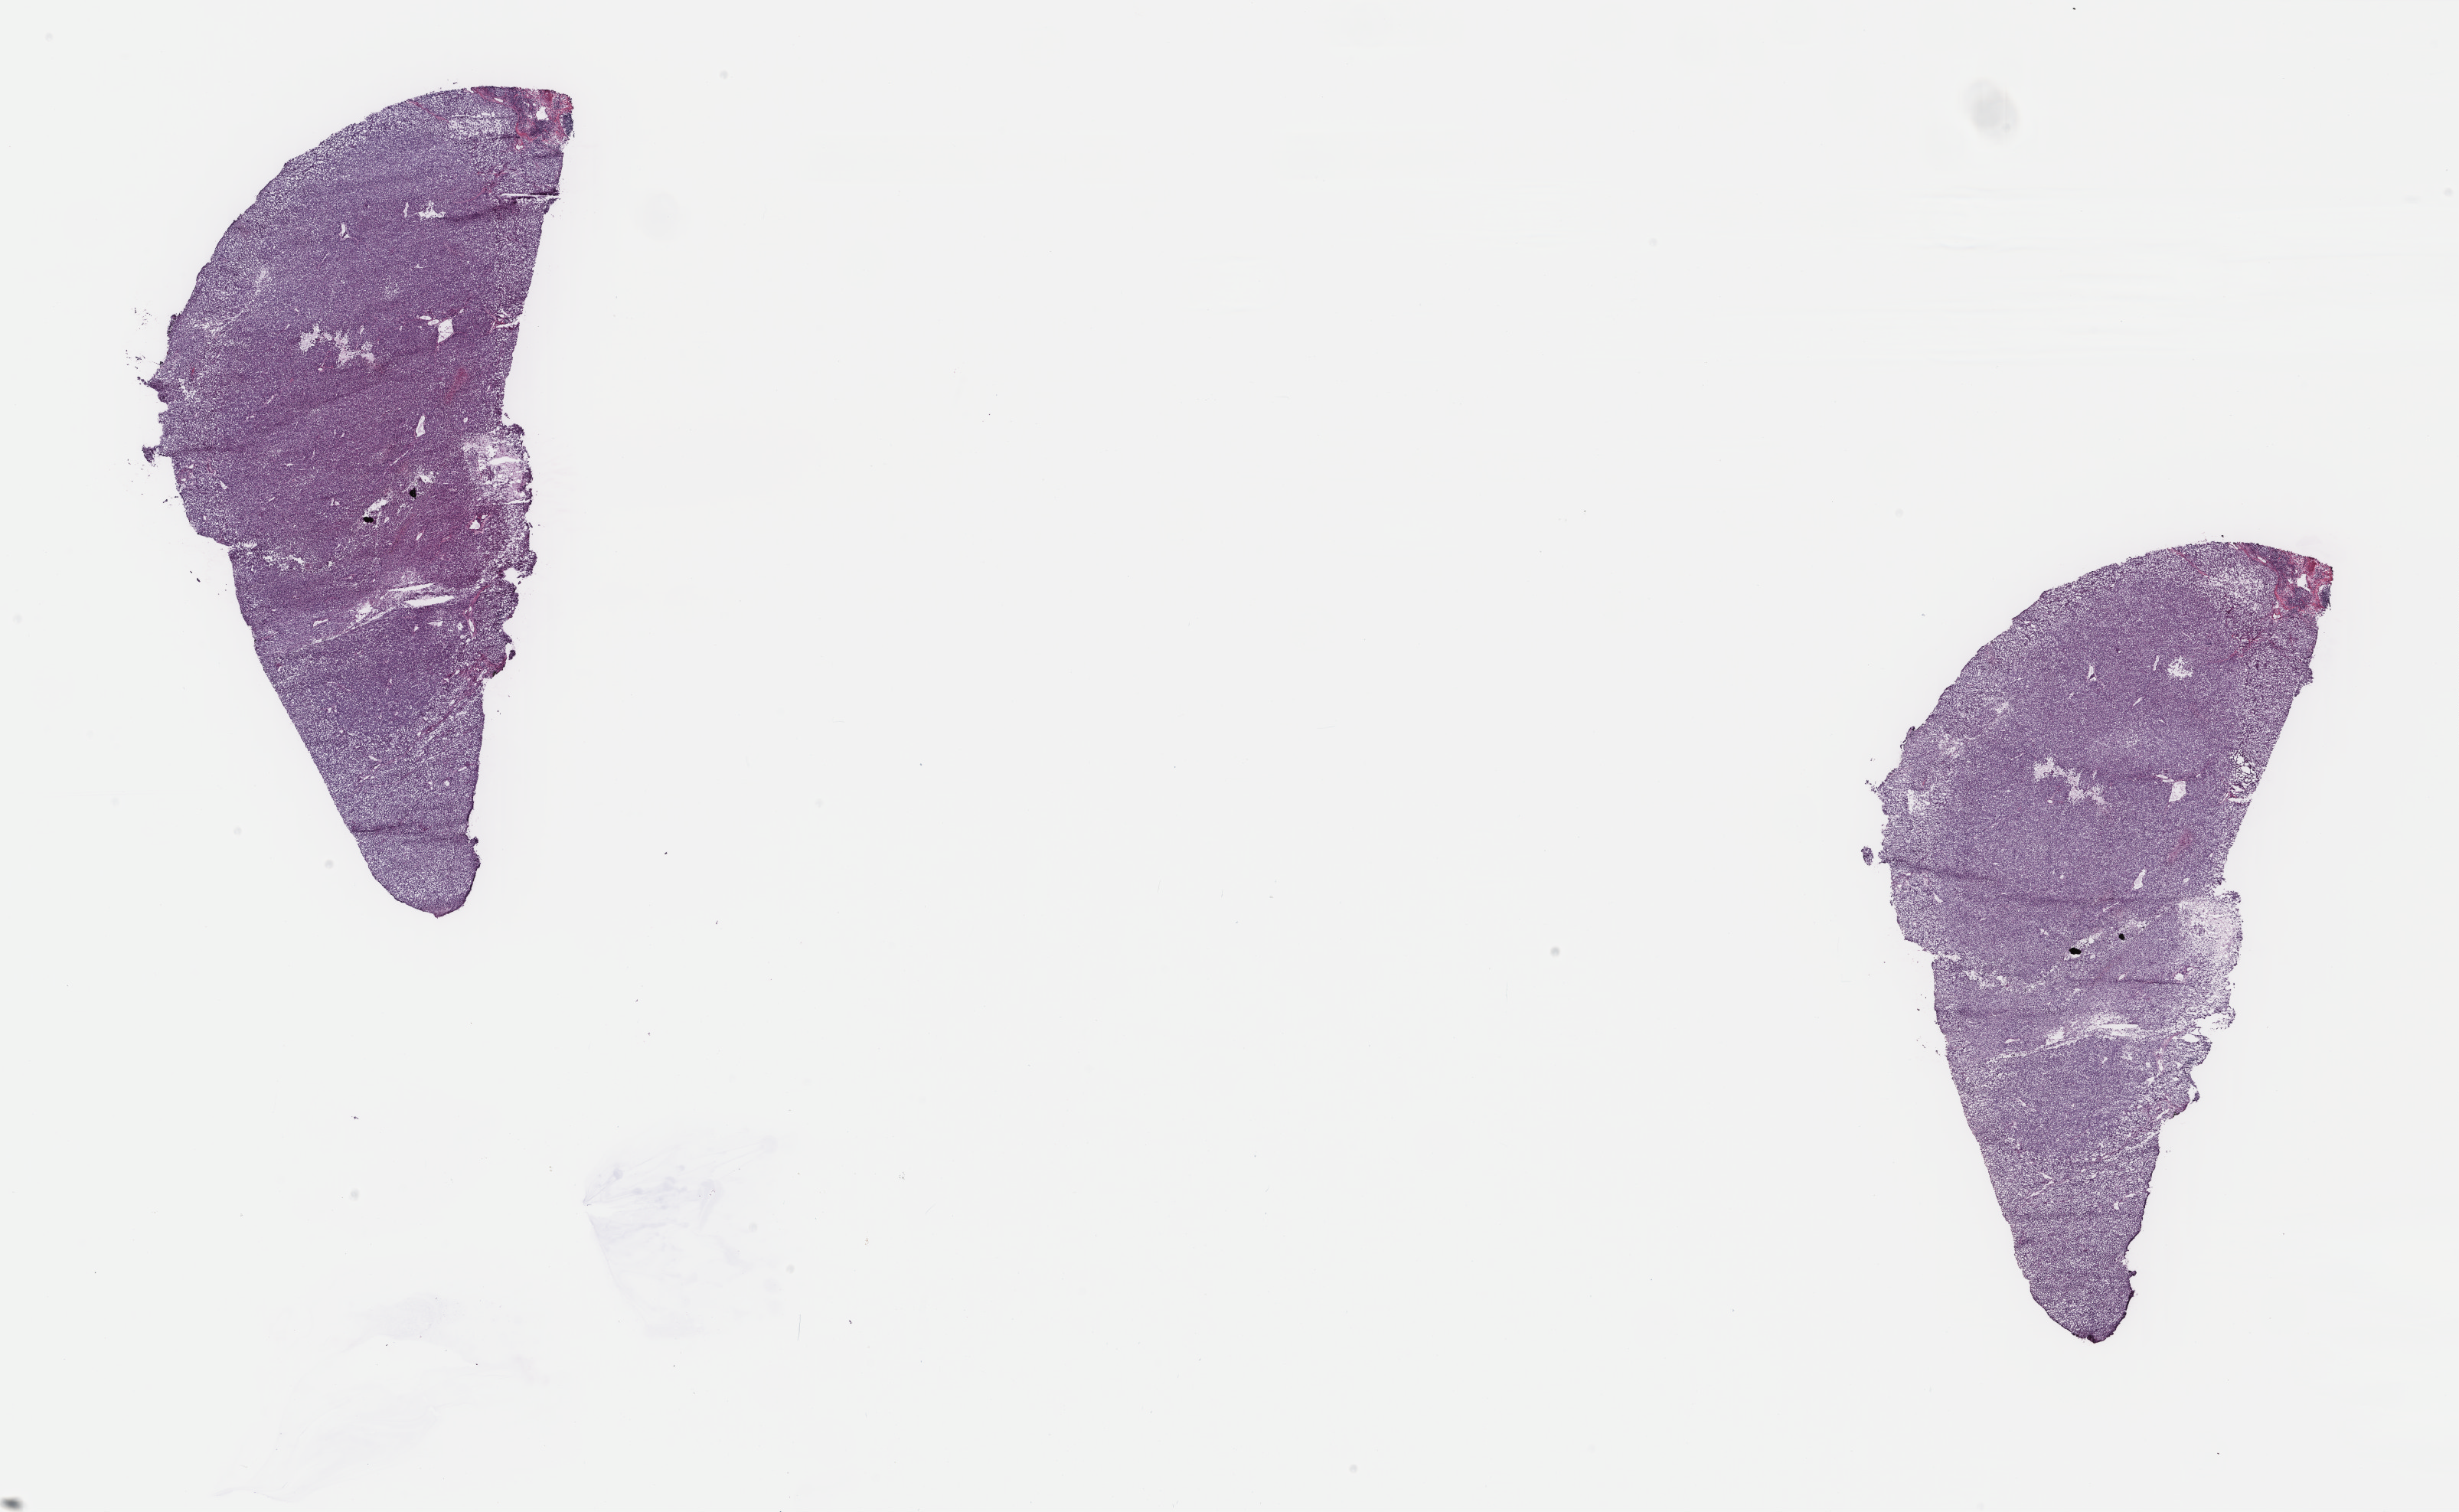
Digitized Hematoxylin and eosin (H&E) stained tissue section (whole slide) — a low-resolution overview of the entire scanned area, about 25.5 x 15.7 mm (acquisition: 40x scan); frozen section from the top of the tissue portion; metastatic tumour sample. Patient: male, age at initial diagnosis 30 years. Composition of this section per pathologist review: tumour cells 98%, tumour nuclei 97%, normal cells 0%, stromal cells 0%, necrosis 2%. Infiltration values recorded for this section: lymphocyte infiltration 0%, monocyte infiltration 0%, neutrophil infiltration 0%.
This section: metastatic tumour tissue. Patient diagnosis: Malignant melanoma, NOS.